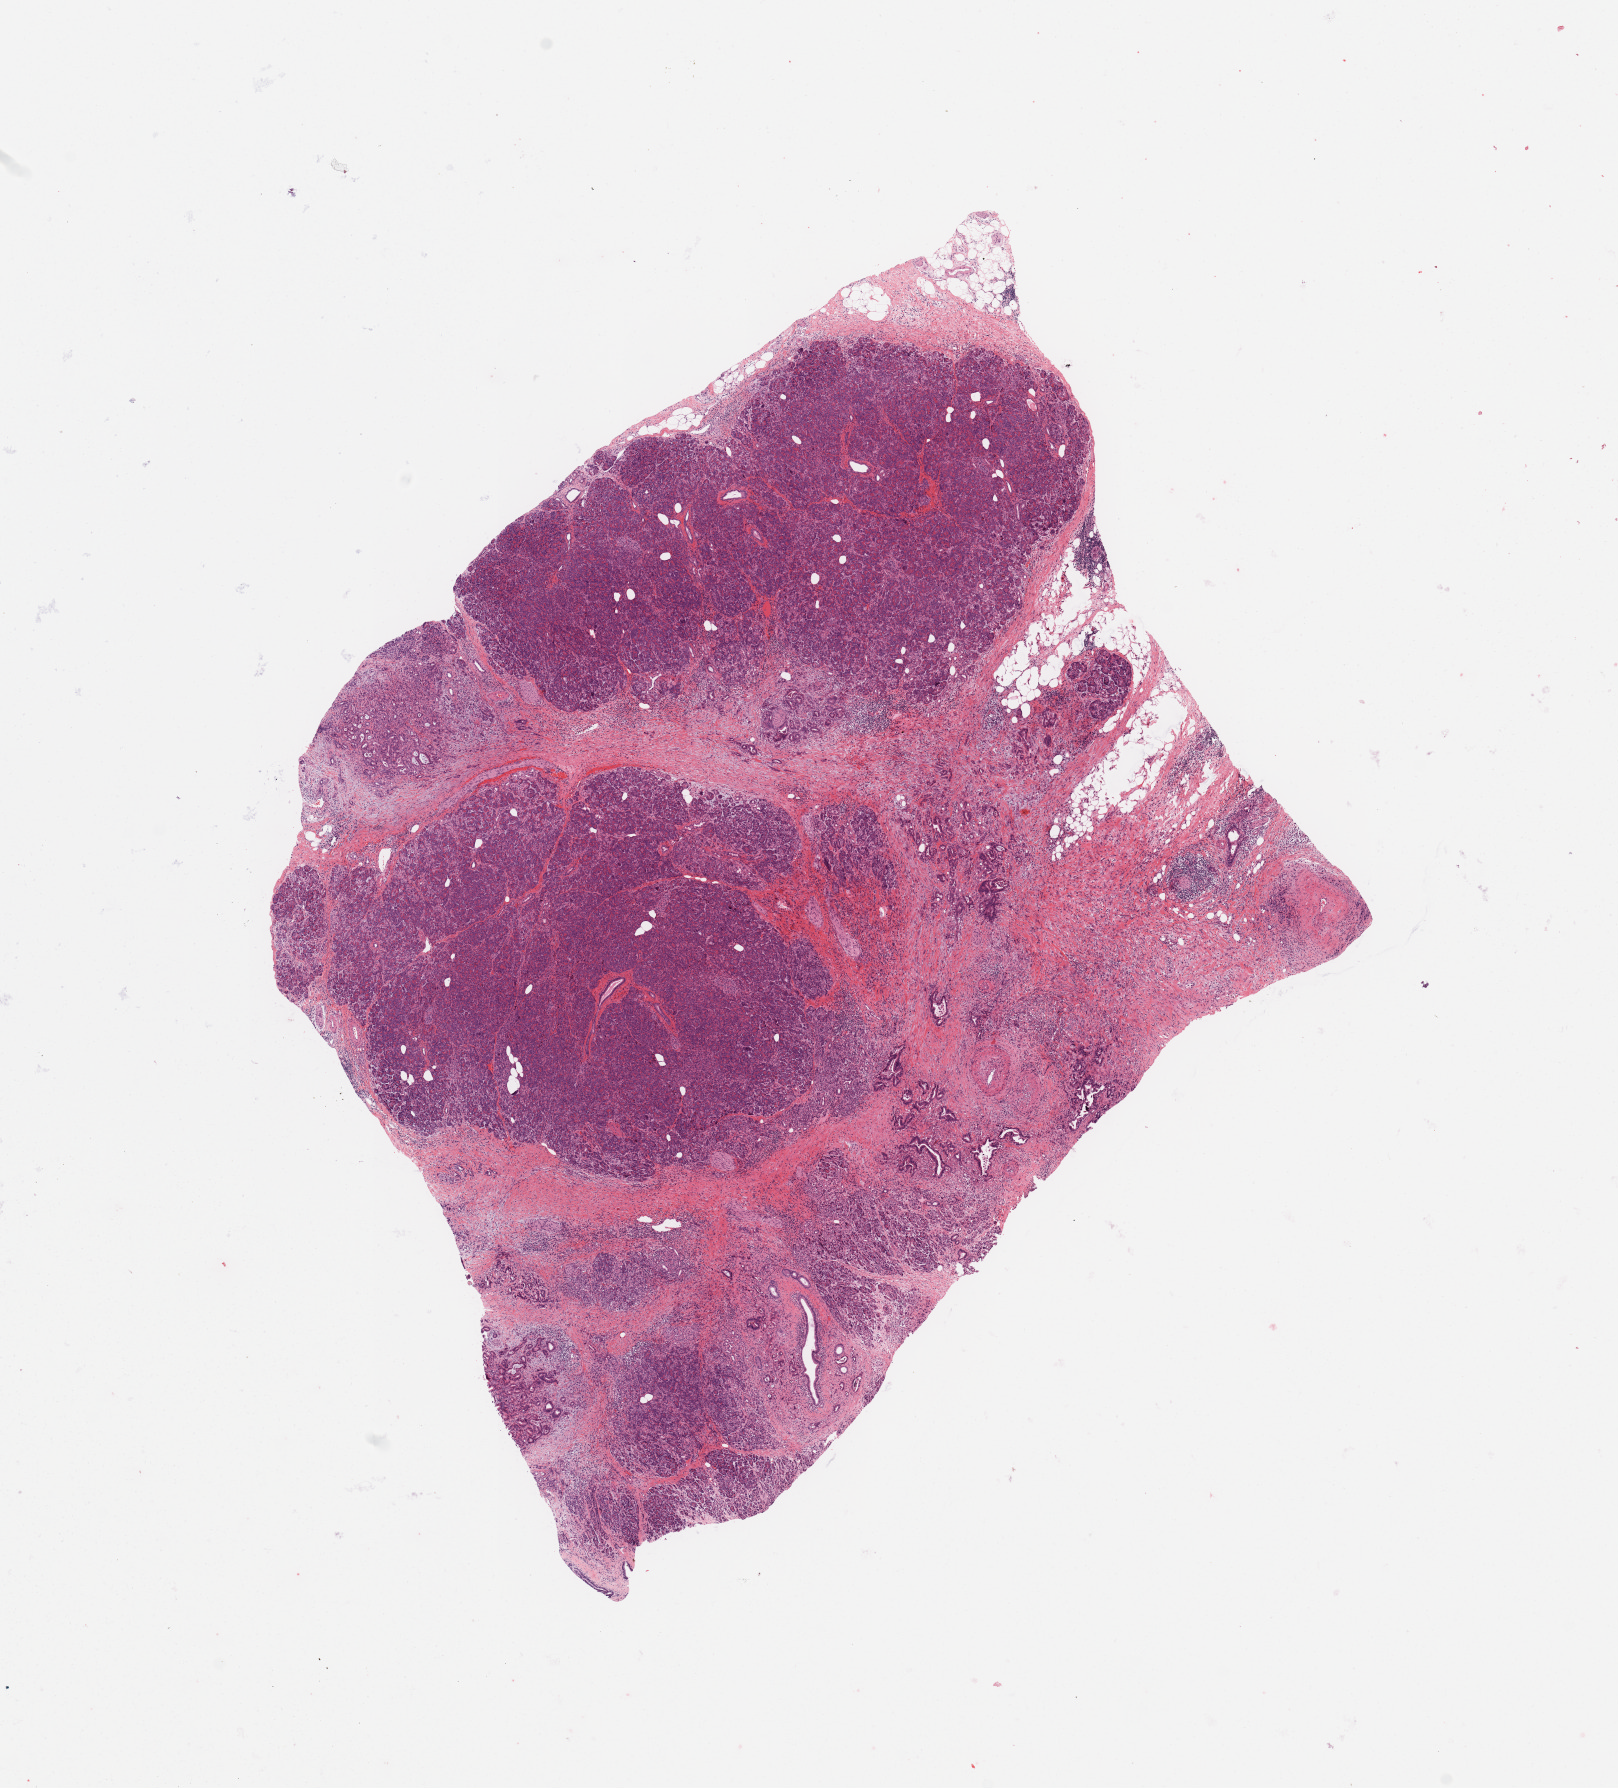
H&E whole-slide image — a low-resolution overview of the entire scanned area, about 12.8 x 14.1 mm; tumour tissue sample, sampled site: pancreas. 69-year-old male patient. Histologic grade: G2 (moderately differentiated). Slide review estimates, as recorded: tumour nuclei 10%, necrosis 0%.
AJCC pathologic stage: IIB. Diagnosis: Infiltrating duct carcinoma, NOS. Primary tumour site (as recorded): head.